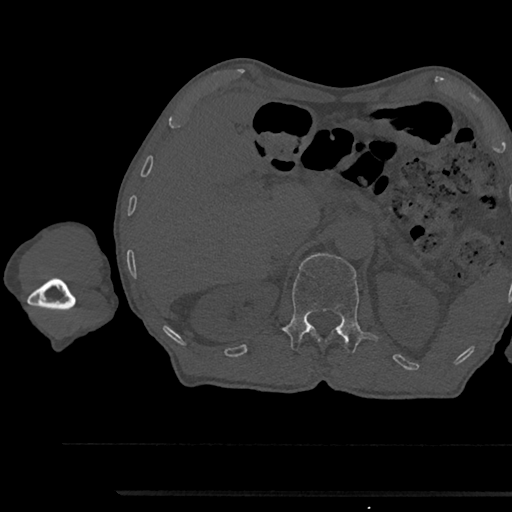
CT including the spine, one axial slice; slice 661 of 797 in the series (ordered by position); reconstruction kernel Br40s/3; 120 kVp; bone window (W 1800 / L 400 HU); 512 × 512 image matrix. Male patient, age 79 years. Case-level facts recorded for this patient, not image findings: primary cancer: prostate.
Structures marked on this image (semi-automatically segmented with operator editing):
- L1 vertebra: bounding box (x1, y1, x2, y2) in pixels: (282, 253, 378, 353)